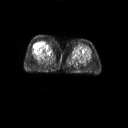
FDG PET of an extremity soft-tissue mass (from a PET/CT study), one axial slice. Position 16 of 267 along the scan axis. 3.27 mm slice thickness. 128 × 128 image matrix, field of view 700 × 700 mm. Patient: female, 56 years. From the clinical record (not read from this slice): histological type: malignant solitary fibrous tumor; grade: intermediate; site of the primary tumour: right thigh.
Annotated regions visible in this slice (expert contour drawn on MRI and transferred to this co-registered scan by the dataset authors):
- gross tumour volume including surrounding oedema: box from (x=40, y=41) to (x=51, y=49) px